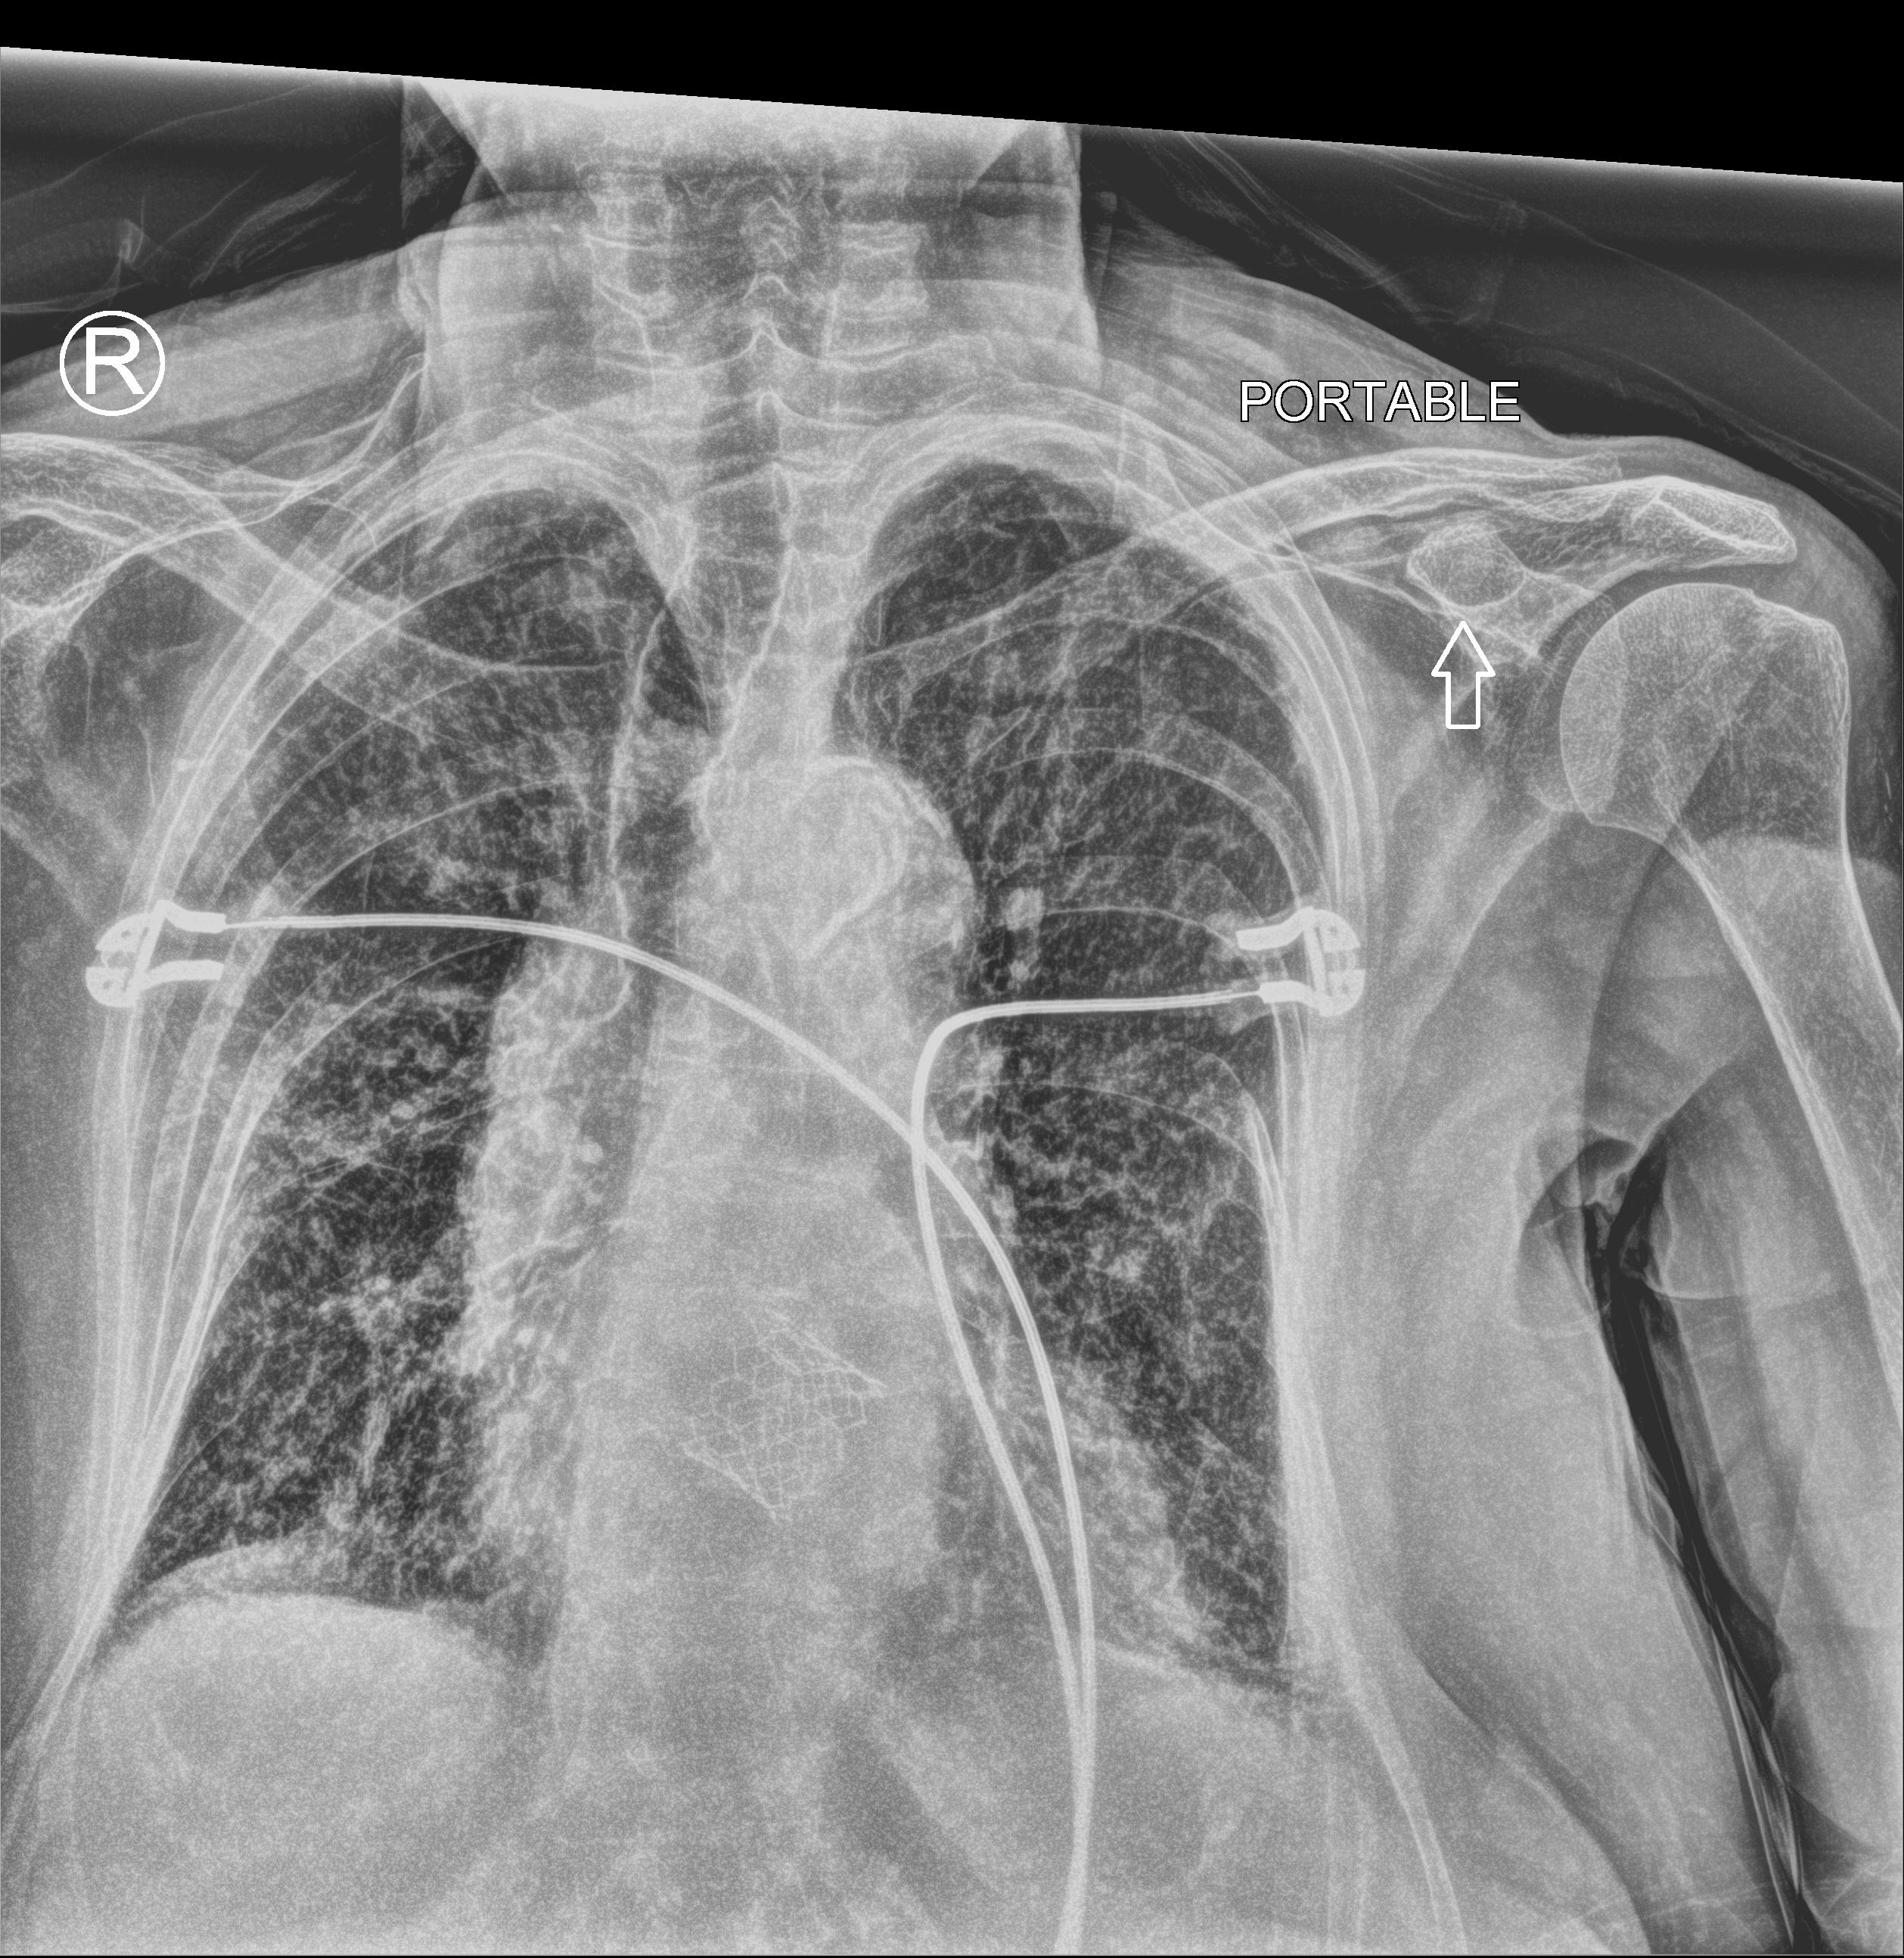
Chest X-ray (portable); anteroposterior (AP) projection. Patient hospitalised with COVID-19; female, aged 75–90 years.
Admission-level facts for this patient (not findings on this image; timing relative to this image not recorded):
- COPD (admission record): no